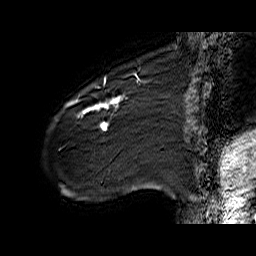
Breast MRI (dynamic contrast-enhanced), one sagittal slice. Position 13 of 60 along the scan axis. Dynamic contrast-enhanced series, time point 2 of 6 at this slice position (early post-contrast). 1.5 T. TE 6.4 ms, TR 32.9 ms. 256 × 256 image matrix, field of view 200 × 200 mm. Female patient. From the clinical record (not read from this slice): setting: breast cancer imaged before/during neoadjuvant chemotherapy; receptor status: HER2-positive.
Outlined on this slice (semi-automatically segmented with operator editing):
- analysis volume of interest (the breast-tissue region the enhancement analysis was run in; not a lesion): box from (x=61, y=77) to (x=141, y=142) px
- tumour enhancement mask (voxels above the 100 % enhancement threshold inside the analysis volume of interest): (x=65, y=79)–(x=139, y=130)